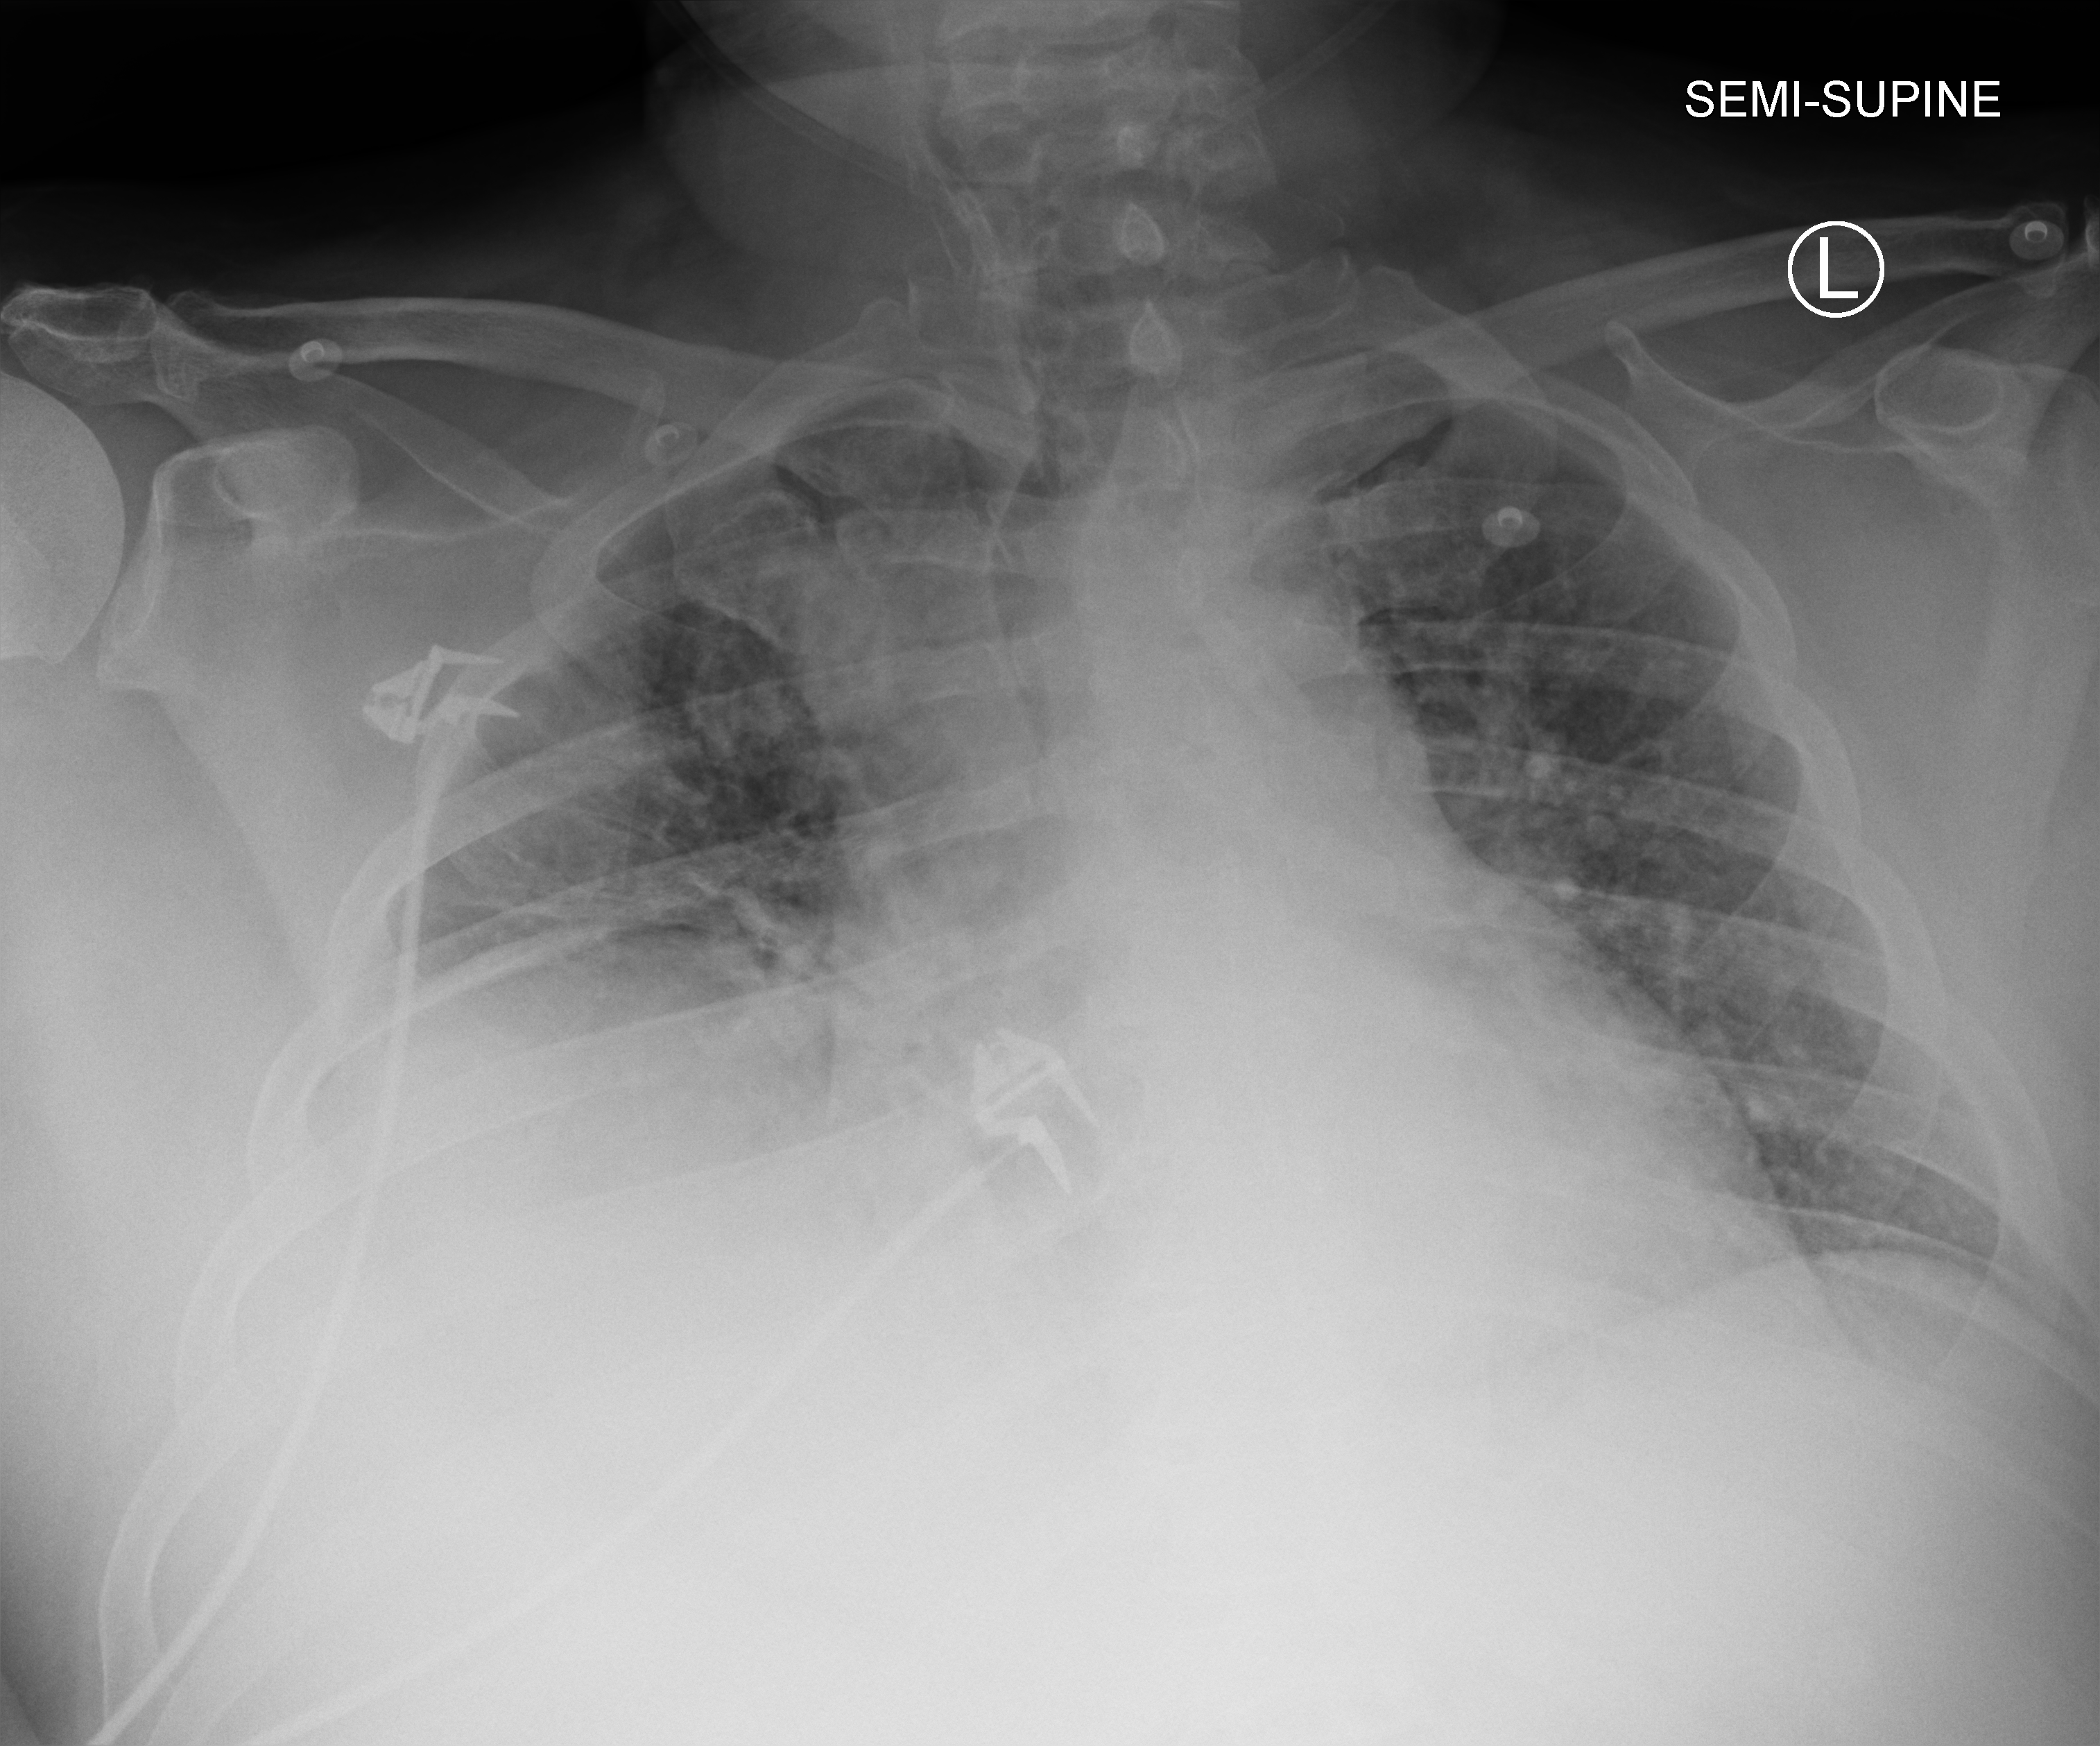
Bedside chest radiograph (computed radiography); anteroposterior (AP) projection. Patient hospitalised with COVID-19; male, aged 18–59 years.
Admission-level facts for this patient (not findings on this image; timing relative to this image not recorded): mechanically ventilated during this hospital stay: yes.